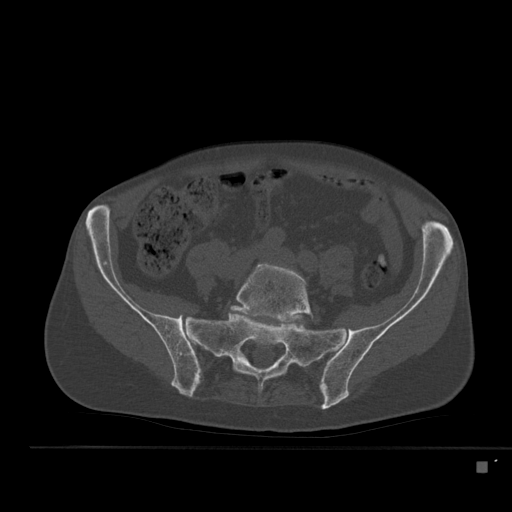
CT including the spine, one axial slice. Slice 115 of 517 in the series (ordered by position). 120 kVp. Bone window (W 1800 / L 400 HU). 1.5 mm slice thickness. 512 × 512 image matrix, field of view 408 × 408 mm. Patient: male, 70 years. Case-level facts recorded for this patient, not image findings: primary cancer: renal; vertebrae with lytic lesions (as recorded): T4, T6, T10, T12, L3, L4, L5.
Outlined on this slice (semi-automatic segmentation, software-assisted and operator-edited):
- L5 vertebra: bounding box (x1, y1, x2, y2) in pixels: (229, 263, 314, 323)